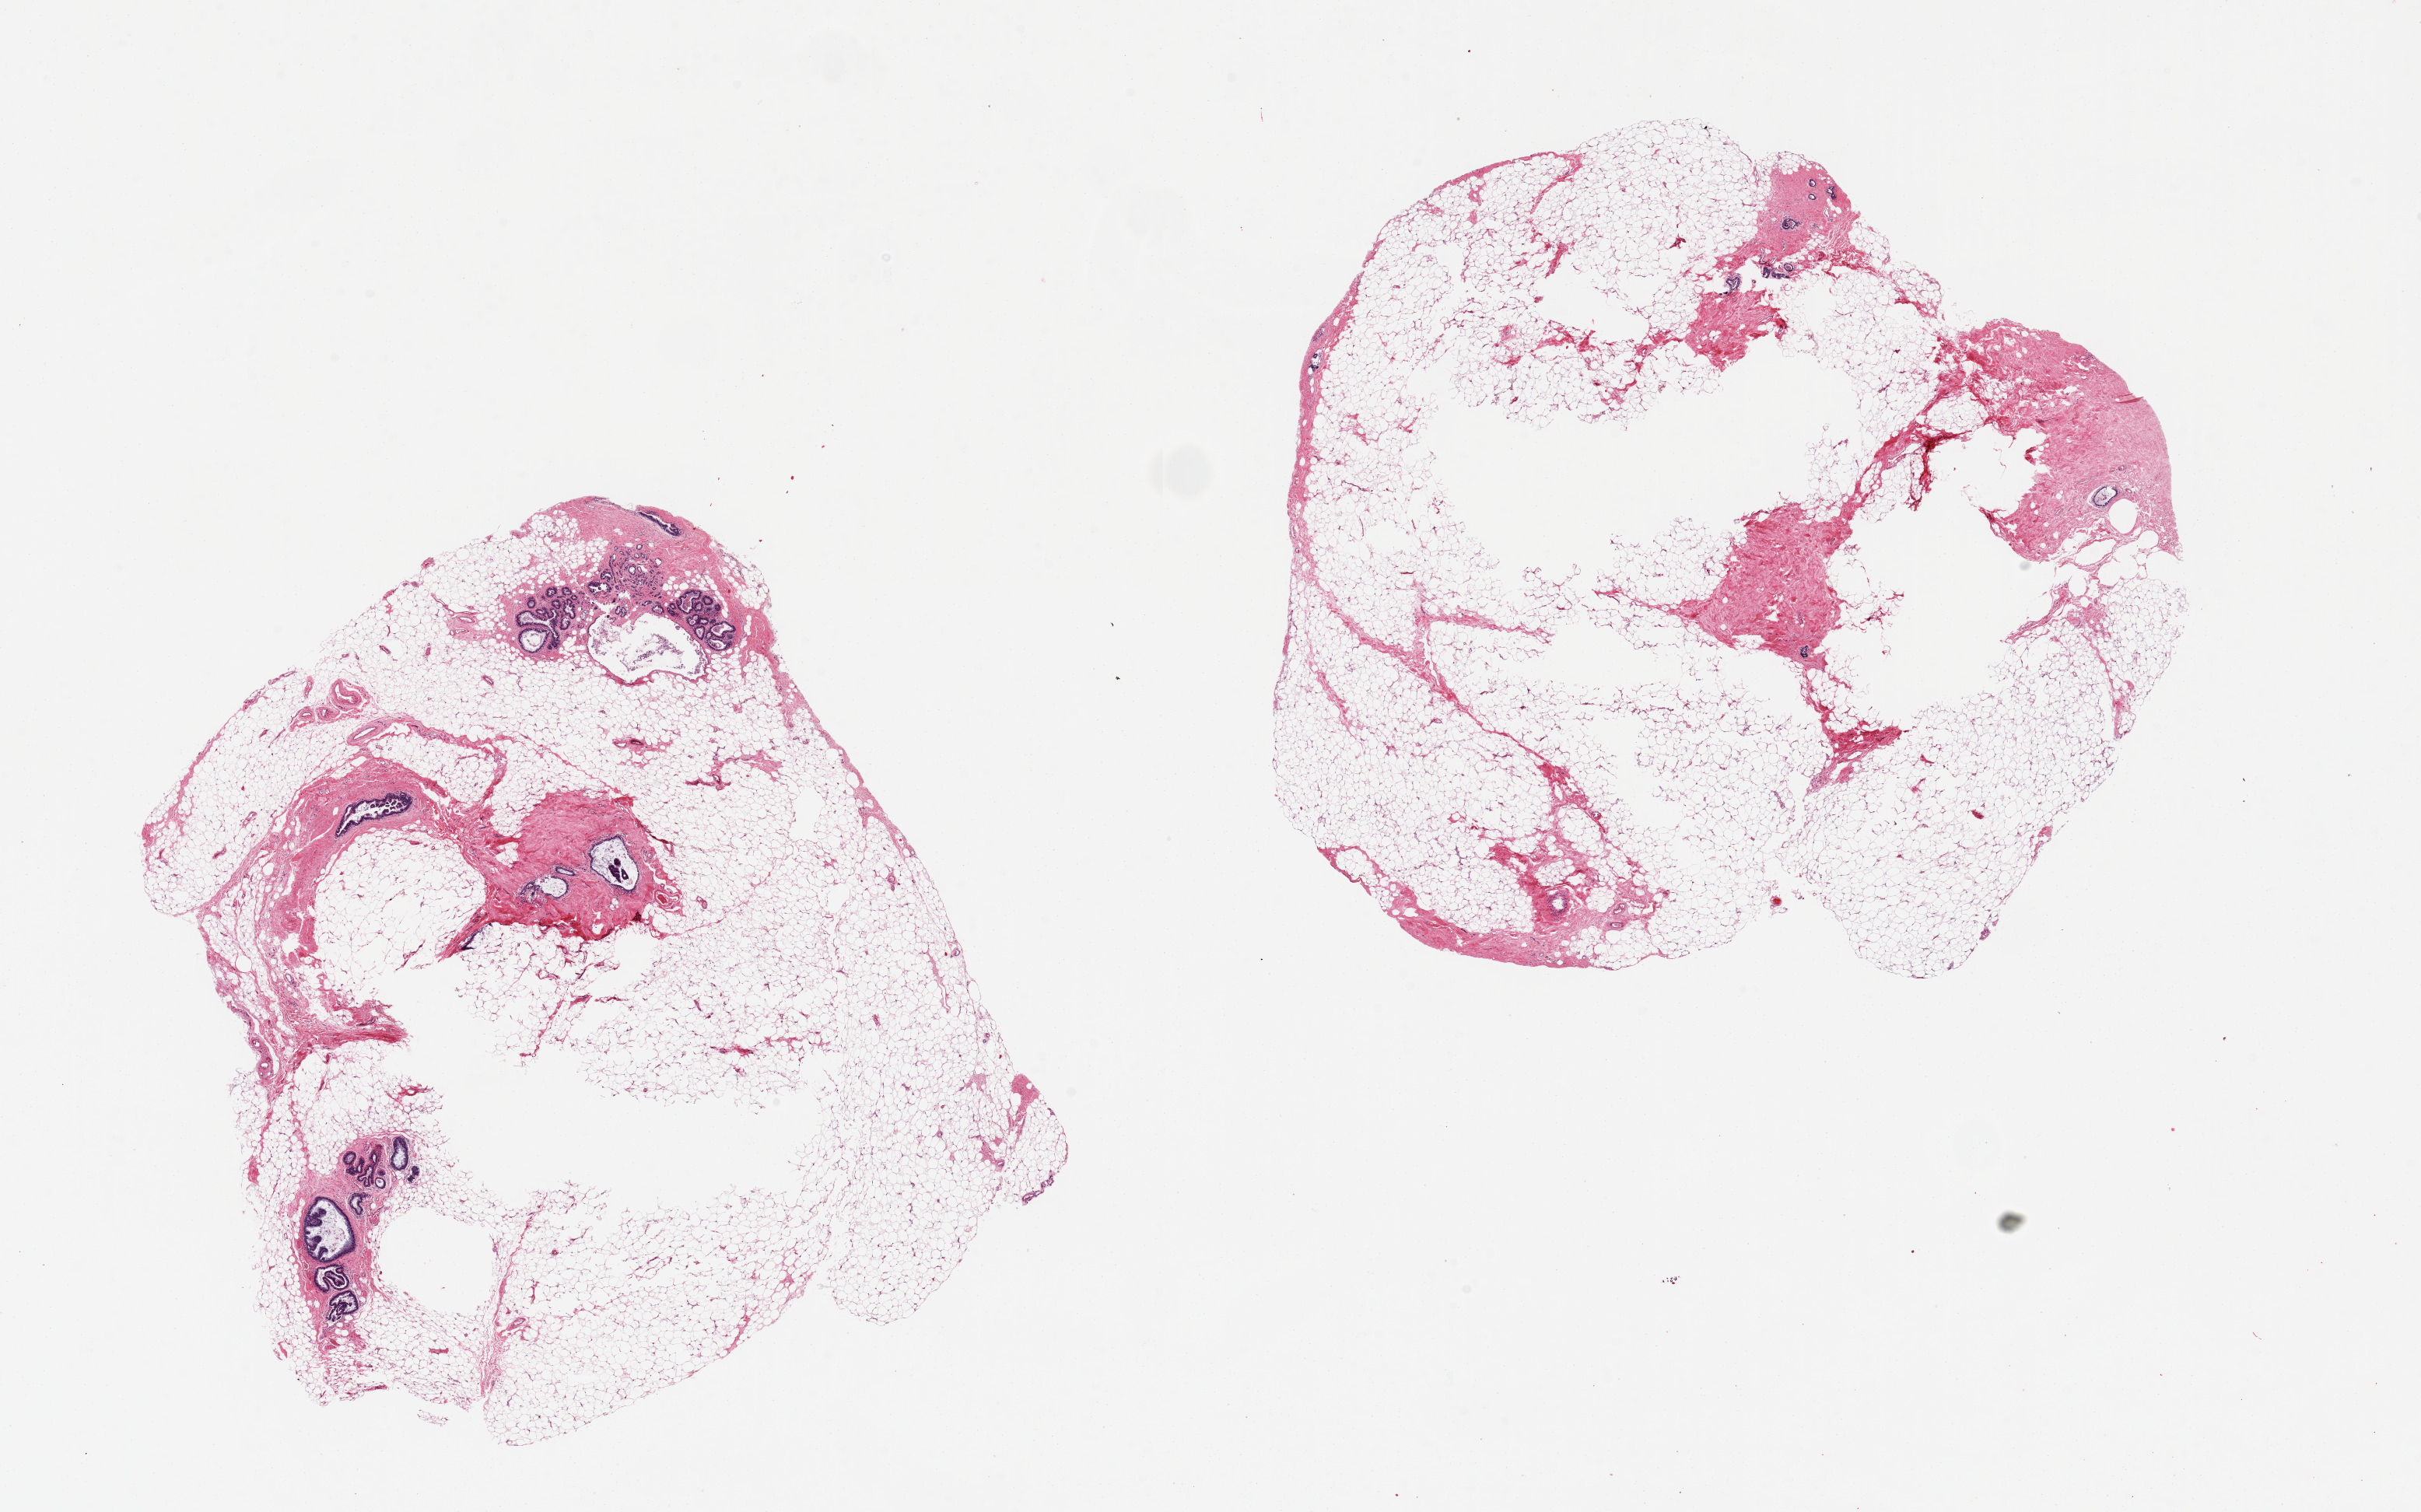
H&E whole-slide image, brightfield, shown as a low-resolution overview of the whole scanned area (about 24.6 x 15.4 mm), PAXgene-fixed, paraffin-embedded tissue, sampled site (target tissue): breast, donor tissue sample. Donor: female.
• review note (as recorded): 2 pieces, 8x8 & 9x9 mm; ducts and lobules present; 80% adipose tissue